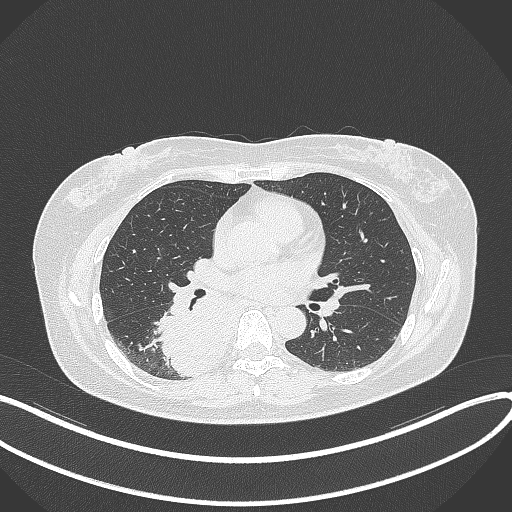
Chest CT, one axial slice. Slice 187 of 331 in the series (ordered by position). Reconstruction kernel B70f. 120 kVp. Lung window (W 1500 / L -600 HU). 1 mm slice thickness. 512 × 512 image matrix. Female patient, age 54 years. Case-level facts recorded for this patient, not image findings: clinical TNM (as recorded): T4 N0 M0.
Annotated regions visible in this slice (bounding box drawn by a radiologist):
- lung tumour (recorded histology: adenocarcinoma): bounding box <156,282,228,375> (left, top, right, bottom; pixels)